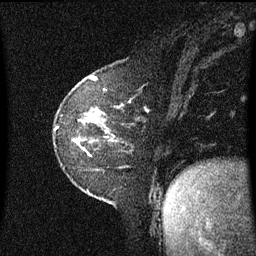
Breast MRI (dynamic contrast-enhanced), one sagittal slice; dynamic contrast-enhanced series, image 2 of 3 at this slice position (ordered by acquisition); 1.5 T; TE 4.2 ms, TR 8.4 ms; 256 × 256 image matrix, field of view 210 × 210 mm. Female patient, age 60 years. From the clinical record (not read from this slice): setting: breast cancer imaged before/during neoadjuvant chemotherapy; receptor status: triple-negative.
Outlined on this slice (semi-automatically segmented with operator editing):
- analysis volume of interest (the breast-tissue region the enhancement analysis was run in; not a lesion): bounding box [x1, y1, x2, y2] px = [56, 108, 116, 158]
- tumour enhancement mask (voxels above the 70 % enhancement threshold inside the analysis volume of interest): [97, 109, 99, 112]